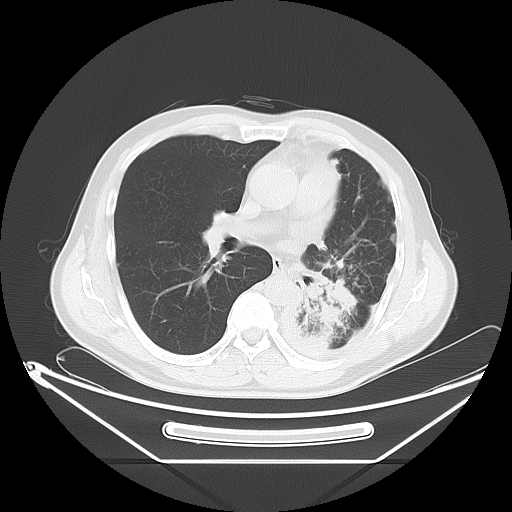
Chest CT, one axial slice. Slice 34 of 63 in the series (ordered by position). Reconstruction kernel LUNG. 120 kVp. Lung window (W 1500 / L -600 HU). 5 mm slice thickness. 512 × 512 image matrix. Patient: male, 60 years. Case-level facts recorded for this patient, not image findings: clinical TNM (as recorded): T4 N1 M1.
Annotated regions visible in this slice (rectangle marked by the reading radiologist):
- lung tumour (recorded histology: adenocarcinoma): bounding box (x1, y1, x2, y2) in pixels: (291, 263, 362, 344)